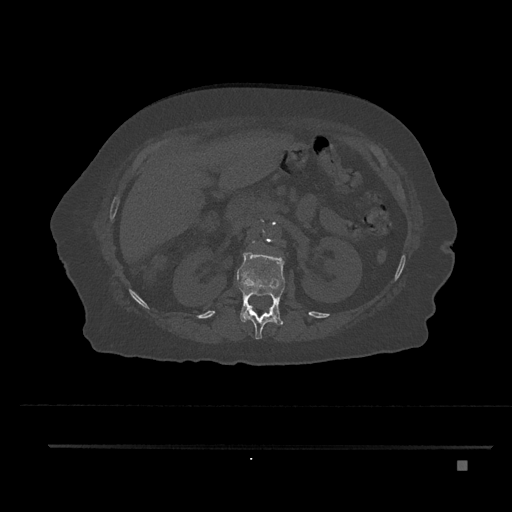
CT including the spine, one axial slice. Slice 235 of 797 in the series (ordered by position). Reconstruction kernel Br40s/3. 120 kVp. Bone window (W 1800 / L 400 HU). 0.5 mm slice thickness. 512 × 512 image matrix, field of view 437 × 437 mm. Patient: female, 76 years. From the clinical record (not read from this slice): primary cancer: lung; vertebrae with lytic lesions (as recorded): T11, L3.
Annotated regions visible in this slice (semi-automatic segmentation, software-assisted and operator-edited):
- L1 vertebra: box from (x=237, y=250) to (x=286, y=325) px
- L2 vertebra: (x=253, y=241)–(x=256, y=244)
- T12 vertebra: (x=245, y=306)–(x=275, y=340)